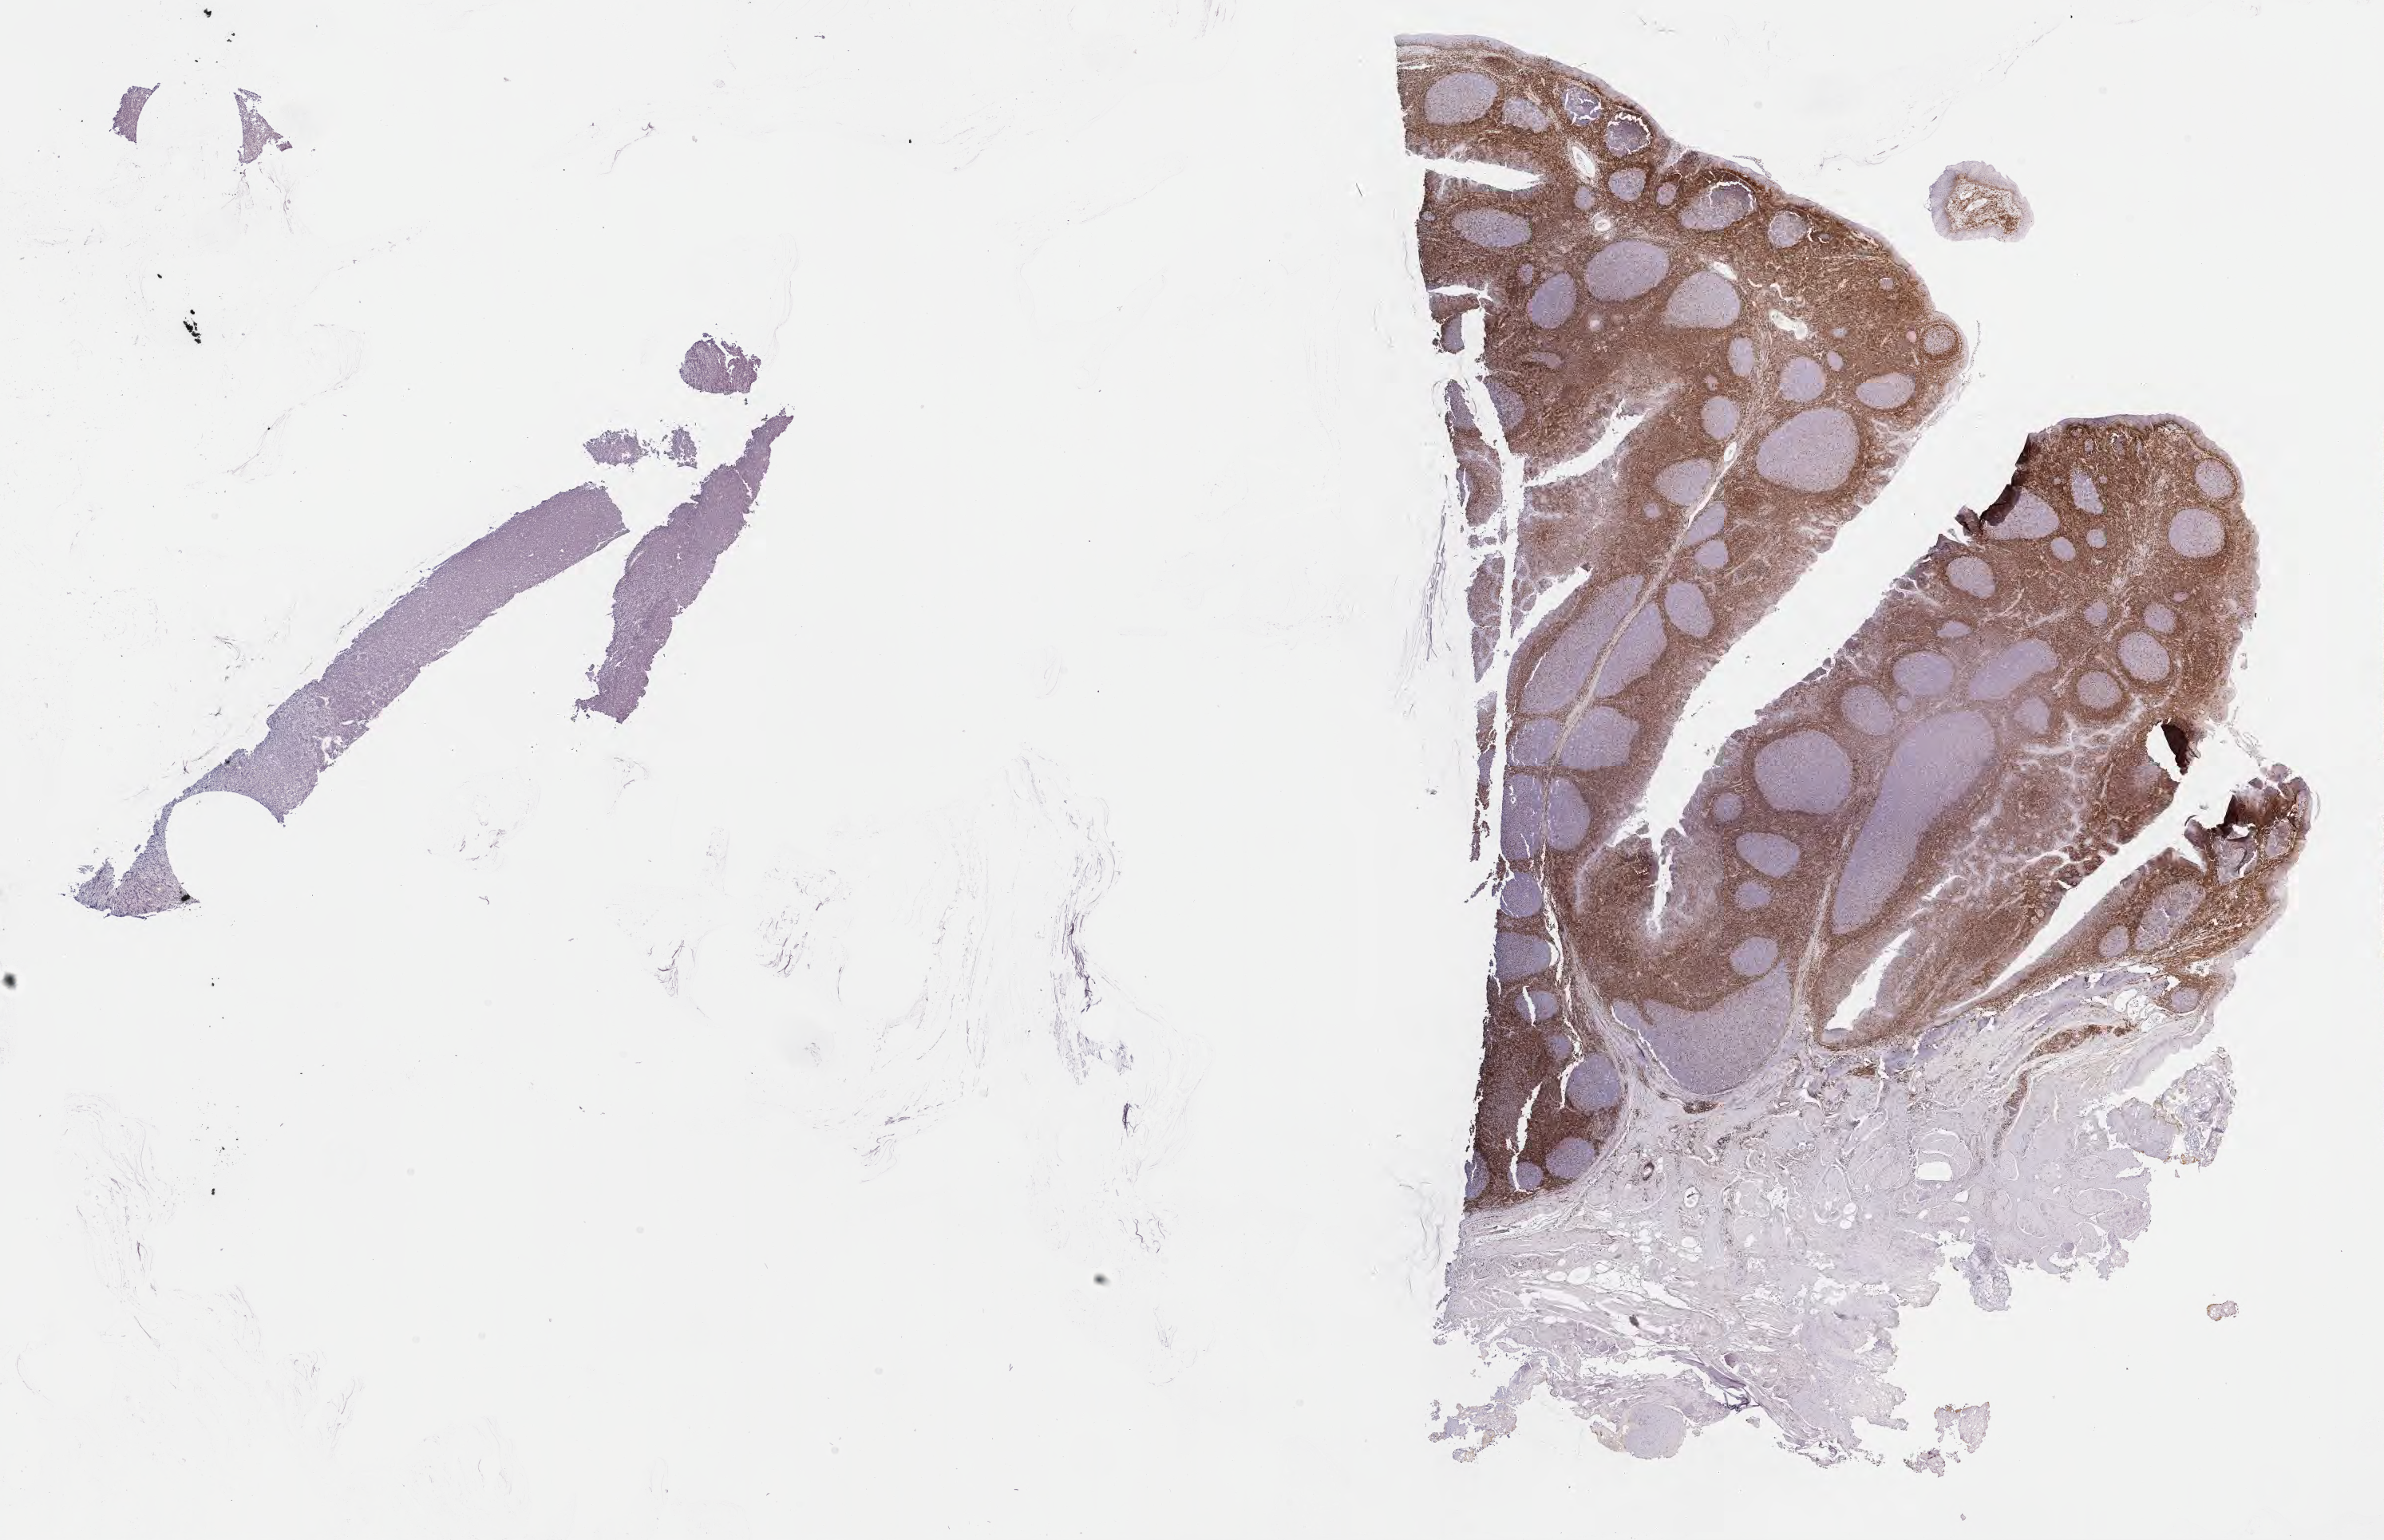
IHC for BCL2, whole-slide image — whole scanned area (about 24.2 x 15.6 mm) shown as a low-resolution overview. Specimen: tumor tissue. Anatomic site: liver. Patient male; age 15 years.
* diagnosis: Burkitt lymphoma, NOS